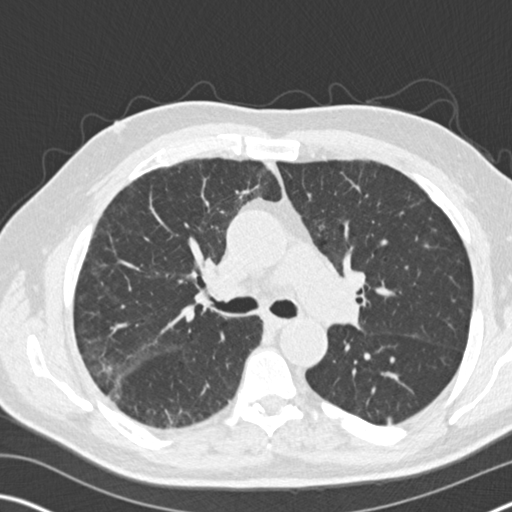
Low-dose screening chest CT, one axial slice; position 106 of 169 along the scan axis; 120 kVp; lung window (W 1500 / L -600 HU); 512 × 512 image matrix, field of view 340 × 340 mm.
Structures marked on this image (manually delineated by an expert):
- lesion 2 (nodule, lower lobe of left lung): bounding box [x1, y1, x2, y2] px = [387, 417, 392, 425]